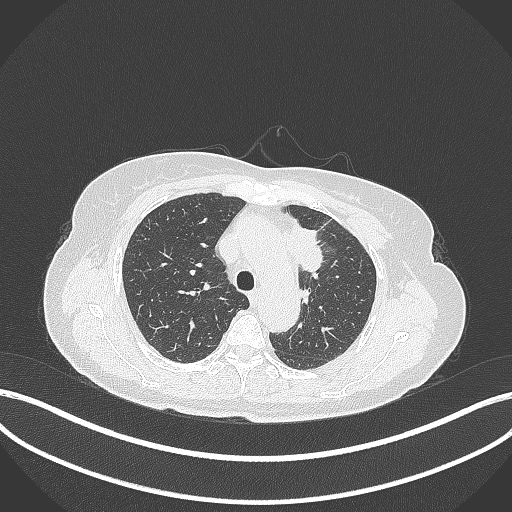
Chest CT, one axial slice. Position 244 of 369 along the scan axis. Reconstruction kernel B70f. 120 kVp. Lung window (W 1500 / L -600 HU). 1 mm slice thickness. 512 × 512 image matrix, field of view 400 × 400 mm. Patient: female, 65 years. From the clinical record (not read from this slice): clinical TNM (as recorded): T2a N0 M0.
Outlined on this slice (rectangle marked by the reading radiologist):
- lung tumour (recorded histology: adenocarcinoma): bounding box (x1, y1, x2, y2) in pixels: (284, 218, 323, 274)